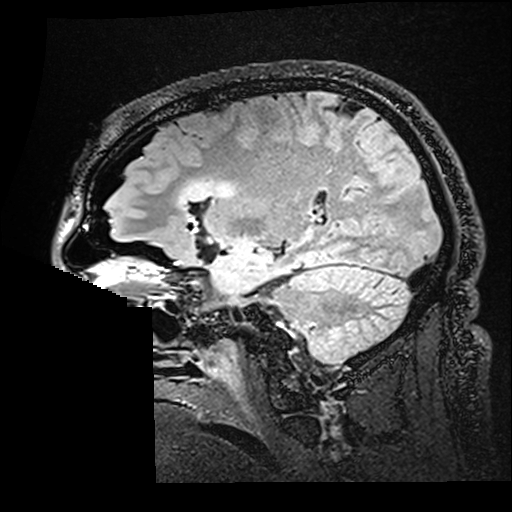
Brain MRI from a brain-tumour surgery series, one sagittal slice; position 113 of 176 along the scan axis; T2 FLAIR; 1 mm slice thickness; 512 × 512 image matrix, field of view 250 × 250 mm. Case-level facts recorded for this patient, not image findings: histopathology: Astrocytoma; WHO grade: 2; IDH mutation: yes; tumour location: Right Insular.
Outlined on this slice (expert manual segmentation):
- residual tumour: box from (x=179, y=180) to (x=236, y=208) px